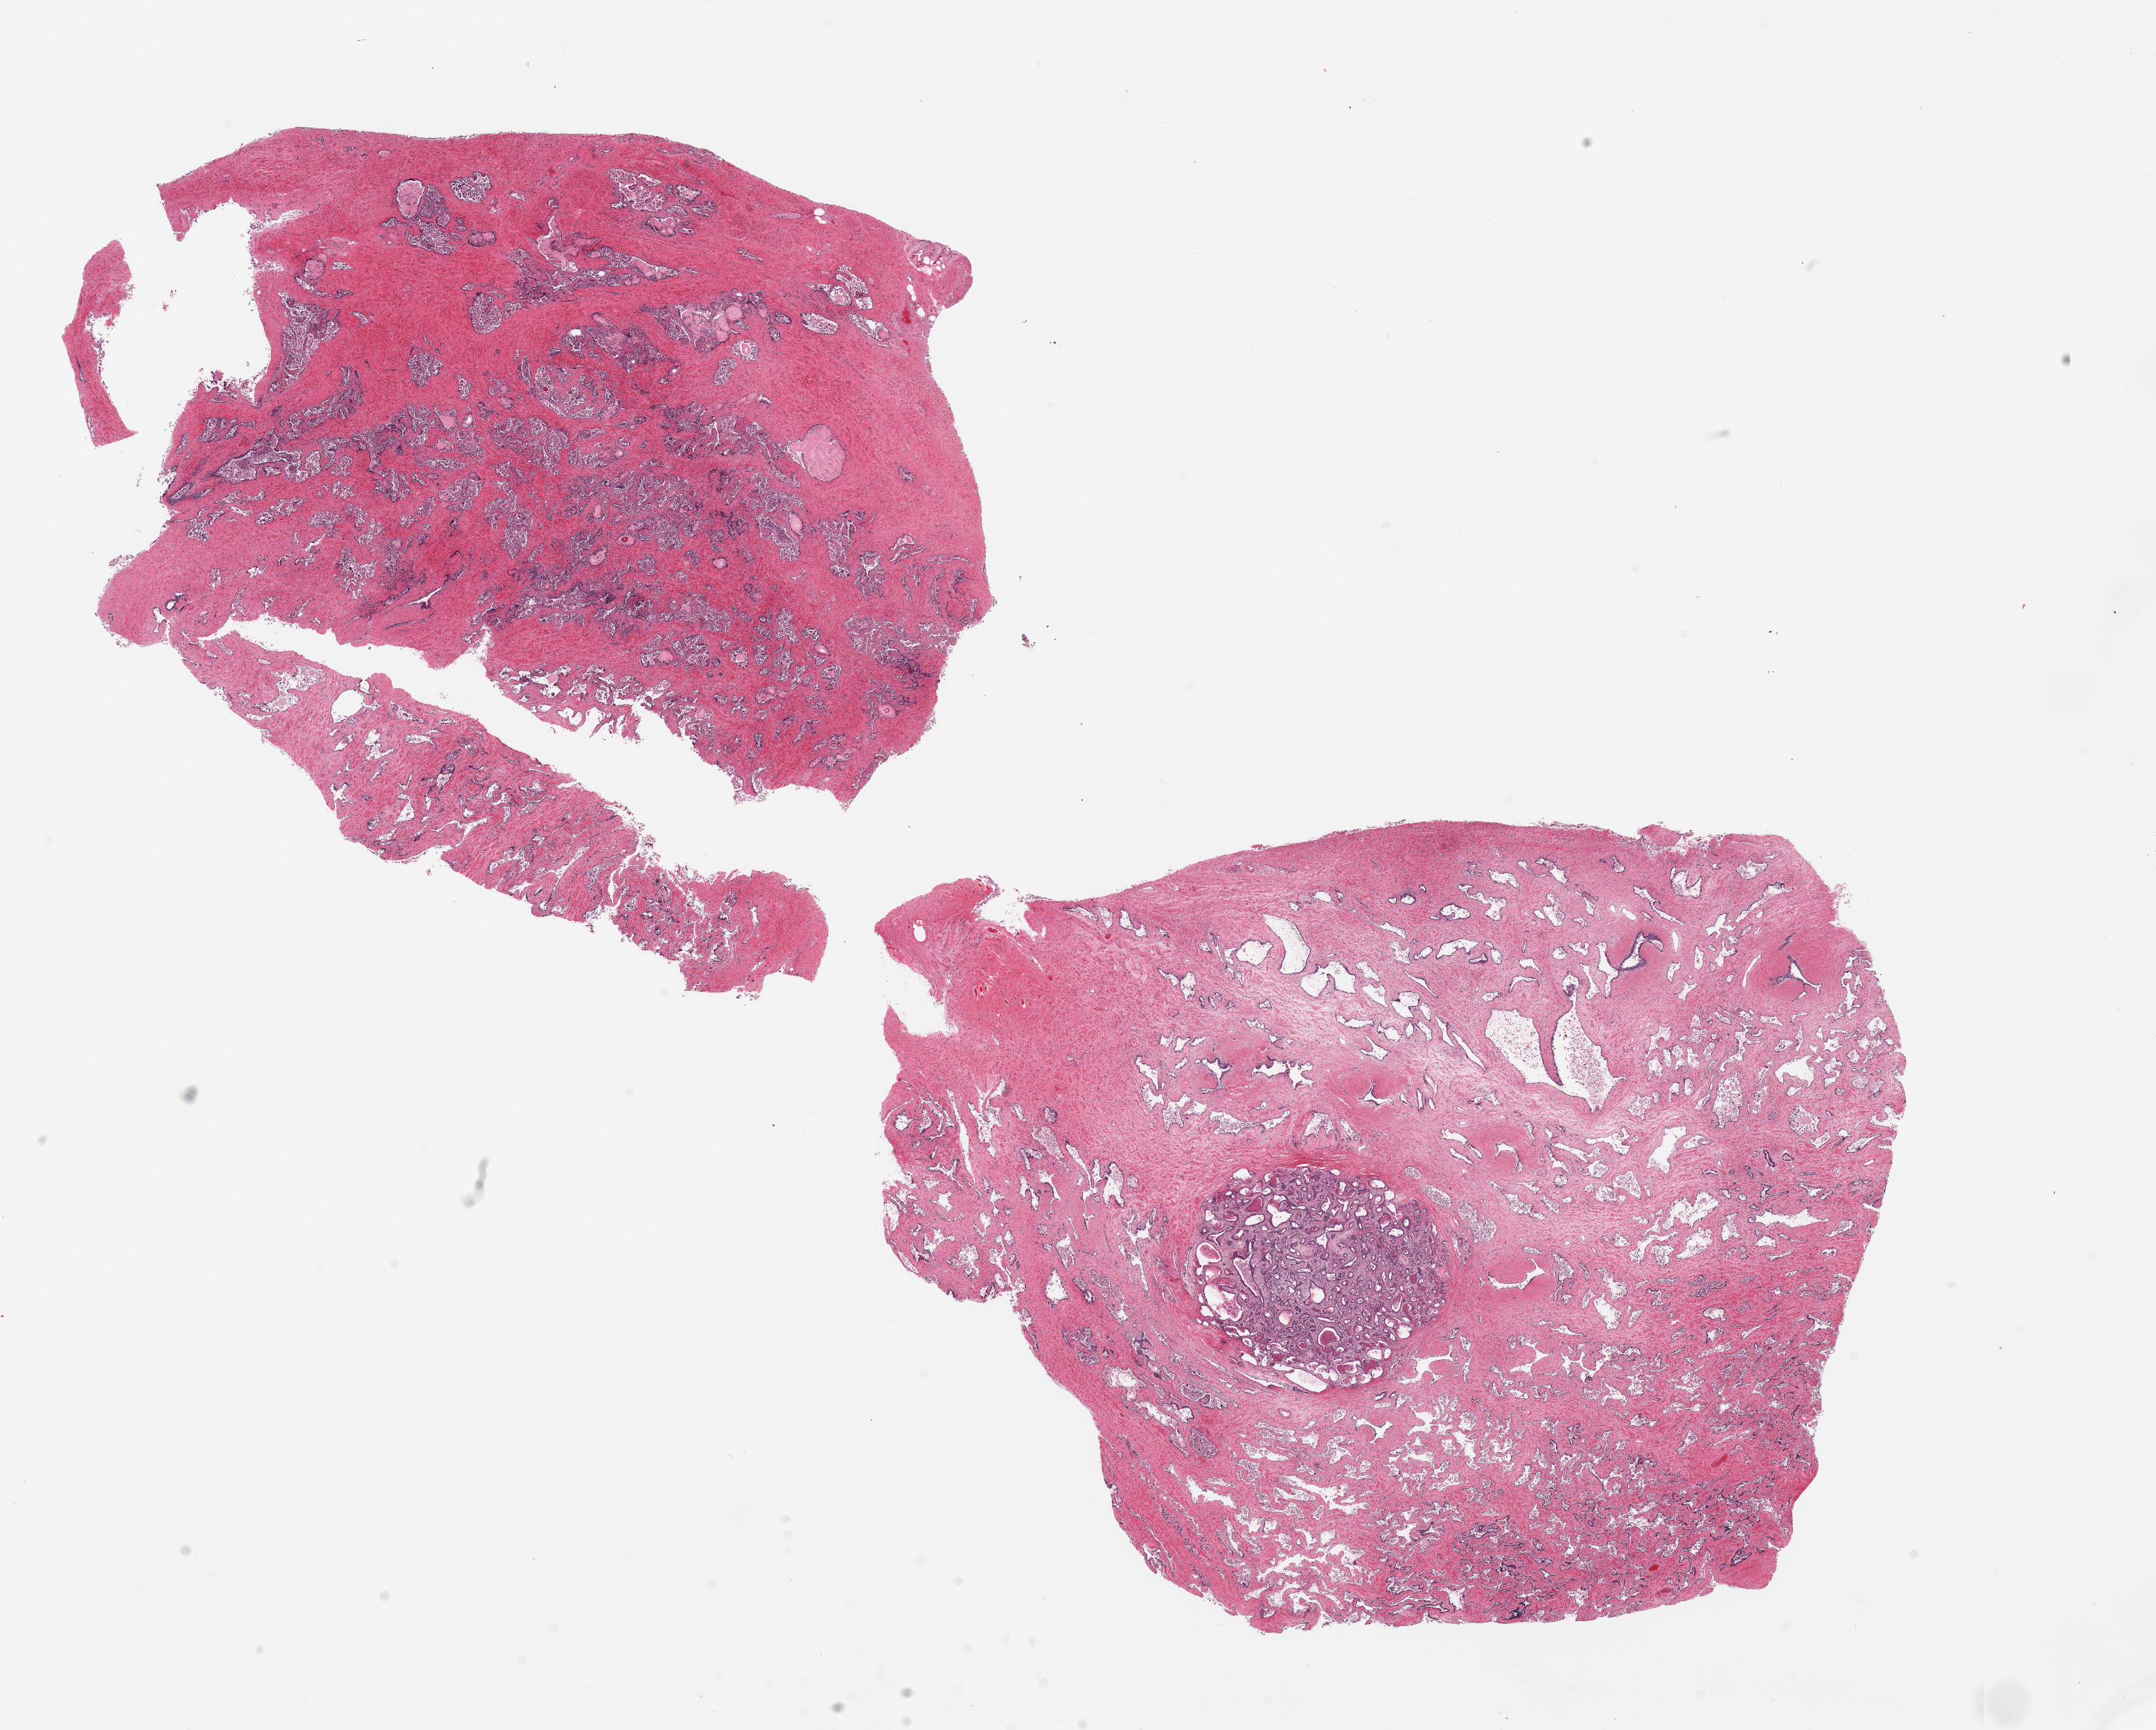
Haematoxylin and eosin whole-slide image, brightfield — a low-resolution overview of the entire scanned area, about 24.6 x 19.7 mm (slide scanned at 20x). PAXgene-fixed paraffin-embedded (PFPE) section. Section of prostate (target tissue). Donor tissue sample. Donor: male.
Reviewer comment on this tissue sample: 2 pieces; 2.8 mm benign hyperplastic glandular and stromal nodule.